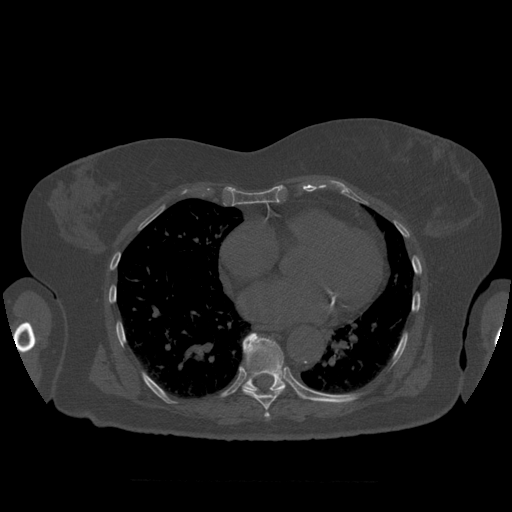
CT including the spine, one axial slice. Position 370 of 399 along the scan axis. Bone window (W 1800 / L 400 HU). 1.25 mm slice thickness. 512 × 512 image matrix. Patient age 81 years. Case-level facts recorded for this patient, not image findings: primary cancer: renal; vertebrae with lytic lesions (as recorded): L1.
Structures marked on this image (semi-automatically segmented with operator editing):
- T7 vertebra: bounding box (x1, y1, x2, y2) in pixels: (265, 412, 270, 418)
- T8 vertebra: (243, 350, 284, 410)
- T9 vertebra: (243, 333, 298, 395)